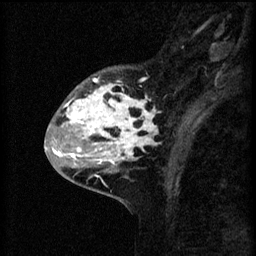
Breast MRI (dynamic contrast-enhanced), one sagittal slice; slice 20 of 60 in the series (ordered by position); 3 images stored at this slice position (order not interpretable as contrast timing); 1.5 T; TE 4.2 ms, TR 8.2 ms; 2 mm slice thickness; 256 × 256 image matrix, field of view 180 × 180 mm. Patient: female, 41 years.
Outlined on this slice (semi-automatically segmented with operator editing):
- analysis volume of interest (the breast-tissue region the enhancement analysis was run in; not a lesion): bounding box [x1, y1, x2, y2] px = [53, 66, 160, 175]
- tumour enhancement mask (voxels above the 70 % enhancement threshold inside the analysis volume of interest): [63, 78, 158, 175]